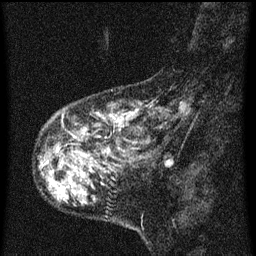
Breast MRI (dynamic contrast-enhanced), one sagittal slice; position 13 of 60 along the scan axis; dynamic contrast-enhanced series, image 2 of 3 at this slice position (ordered by acquisition); 1.5 T; TE 4.2 ms, TR 8 ms; 256 × 256 image matrix, field of view 180 × 180 mm. Female patient, age 55 years.
Annotated regions visible in this slice (semi-automatically segmented with operator editing):
- analysis volume of interest (the breast-tissue region the enhancement analysis was run in; not a lesion): bounding box (x1, y1, x2, y2) in pixels: (38, 100, 179, 159)
- tumour enhancement mask (voxels above the 70 % enhancement threshold inside the analysis volume of interest): (56, 110, 139, 155)